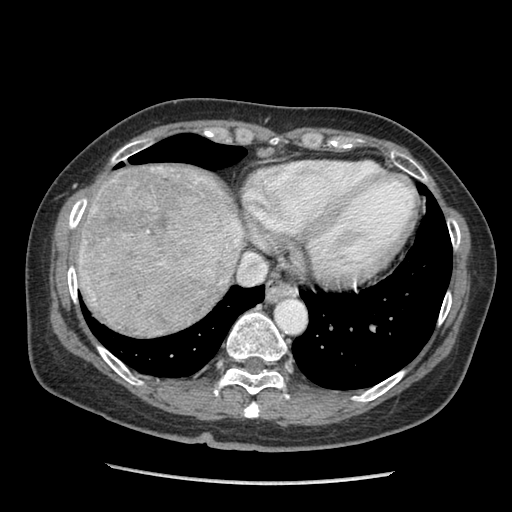
Contrast-enhanced abdominal CT (liver protocol), one axial slice. Slice 83 of 105 in the series (ordered by position). 140 kVp. Soft-tissue window (W 400 / L 40 HU). 2.5 mm slice thickness. 512 × 512 image matrix, field of view 340 × 340 mm. From the clinical record (not read from this slice): diagnosis: hepatocellular carcinoma (patient treated with transarterial chemoembolisation; whether this scan precedes or follows treatment is not stated here); TNM stage (as recorded): Stage-I; Child-Pugh class: A; tumour differentiation: moderately differentiated; tumour nodularity: uninodular.
Annotated regions visible in this slice (semi-automatically segmented with operator editing):
- liver parenchyma outside the tumour (the mass and vessels are separate outlines, so this box may not span the whole liver): bounding box <78,166,244,324> (left, top, right, bottom; pixels)
- mass: <79,167,235,337>
- liver vessels: <235,228,240,242>